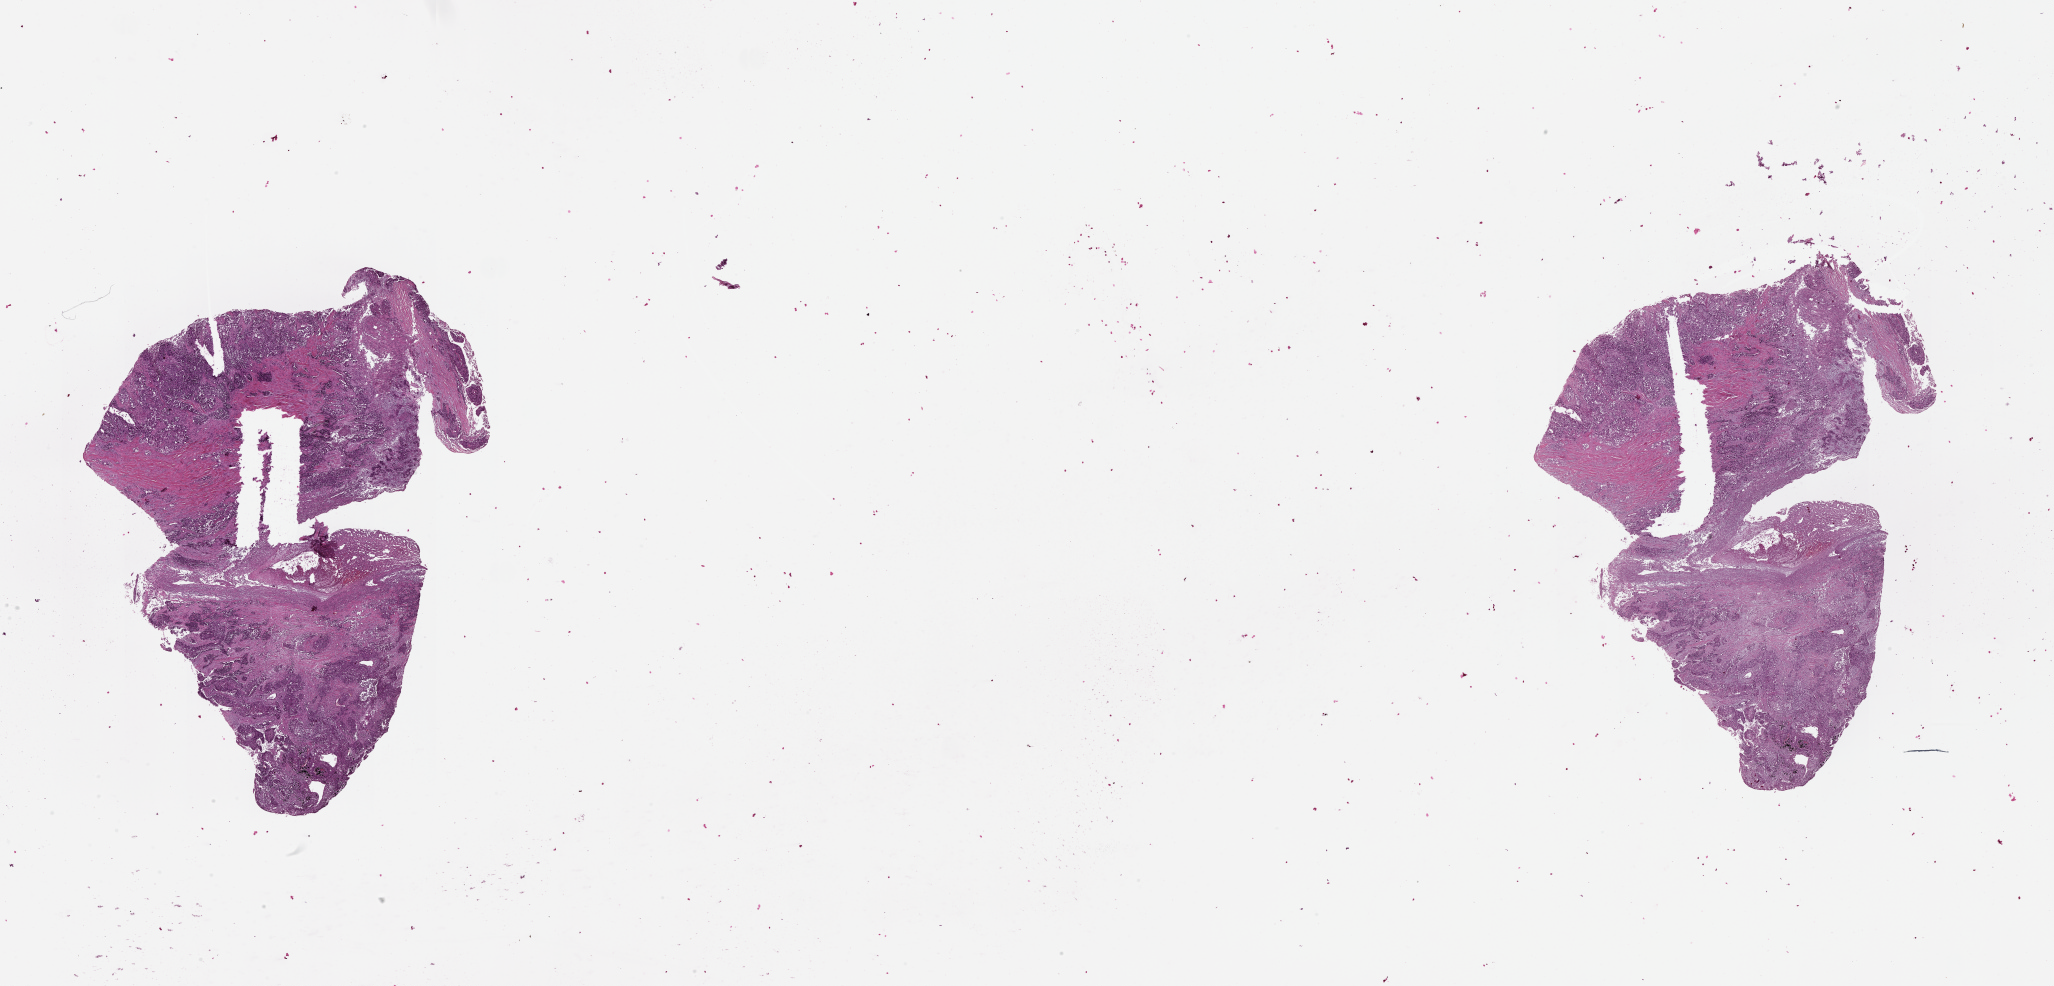
Digitized Hematoxylin and eosin (H&E) stained tissue section (whole slide) — whole scanned area (about 33.1 x 15.9 mm, from a 20x scan) shown as a low-resolution overview; tumour tissue sample, lung. 65-year-old male patient.
Patient diagnosis (cohort enrolment): squamous cell carcinoma (lung).